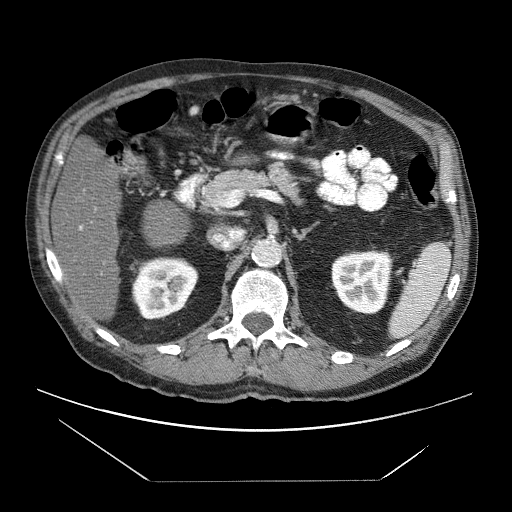
Contrast-enhanced abdominal CT (liver protocol), one axial slice; slice 25 of 83 in the series (ordered by position); reconstruction kernel STANDARD; soft-tissue window (W 400 / L 40 HU); 512 × 512 image matrix. From the clinical record (not read from this slice): diagnosis: hepatocellular carcinoma (patient treated with transarterial chemoembolisation; whether this scan precedes or follows treatment is not stated here); TNM stage (as recorded): Stage-IVB; Child-Pugh class: B; tumour nodularity: uninodular.
Structures marked on this image (semi-automatic segmentation, software-assisted and operator-edited):
- liver parenchyma outside the tumour (the mass and vessels are separate outlines, so this box may not span the whole liver): box from (x=52, y=168) to (x=120, y=320) px
- liver vessels: (x=79, y=226)–(x=82, y=230)